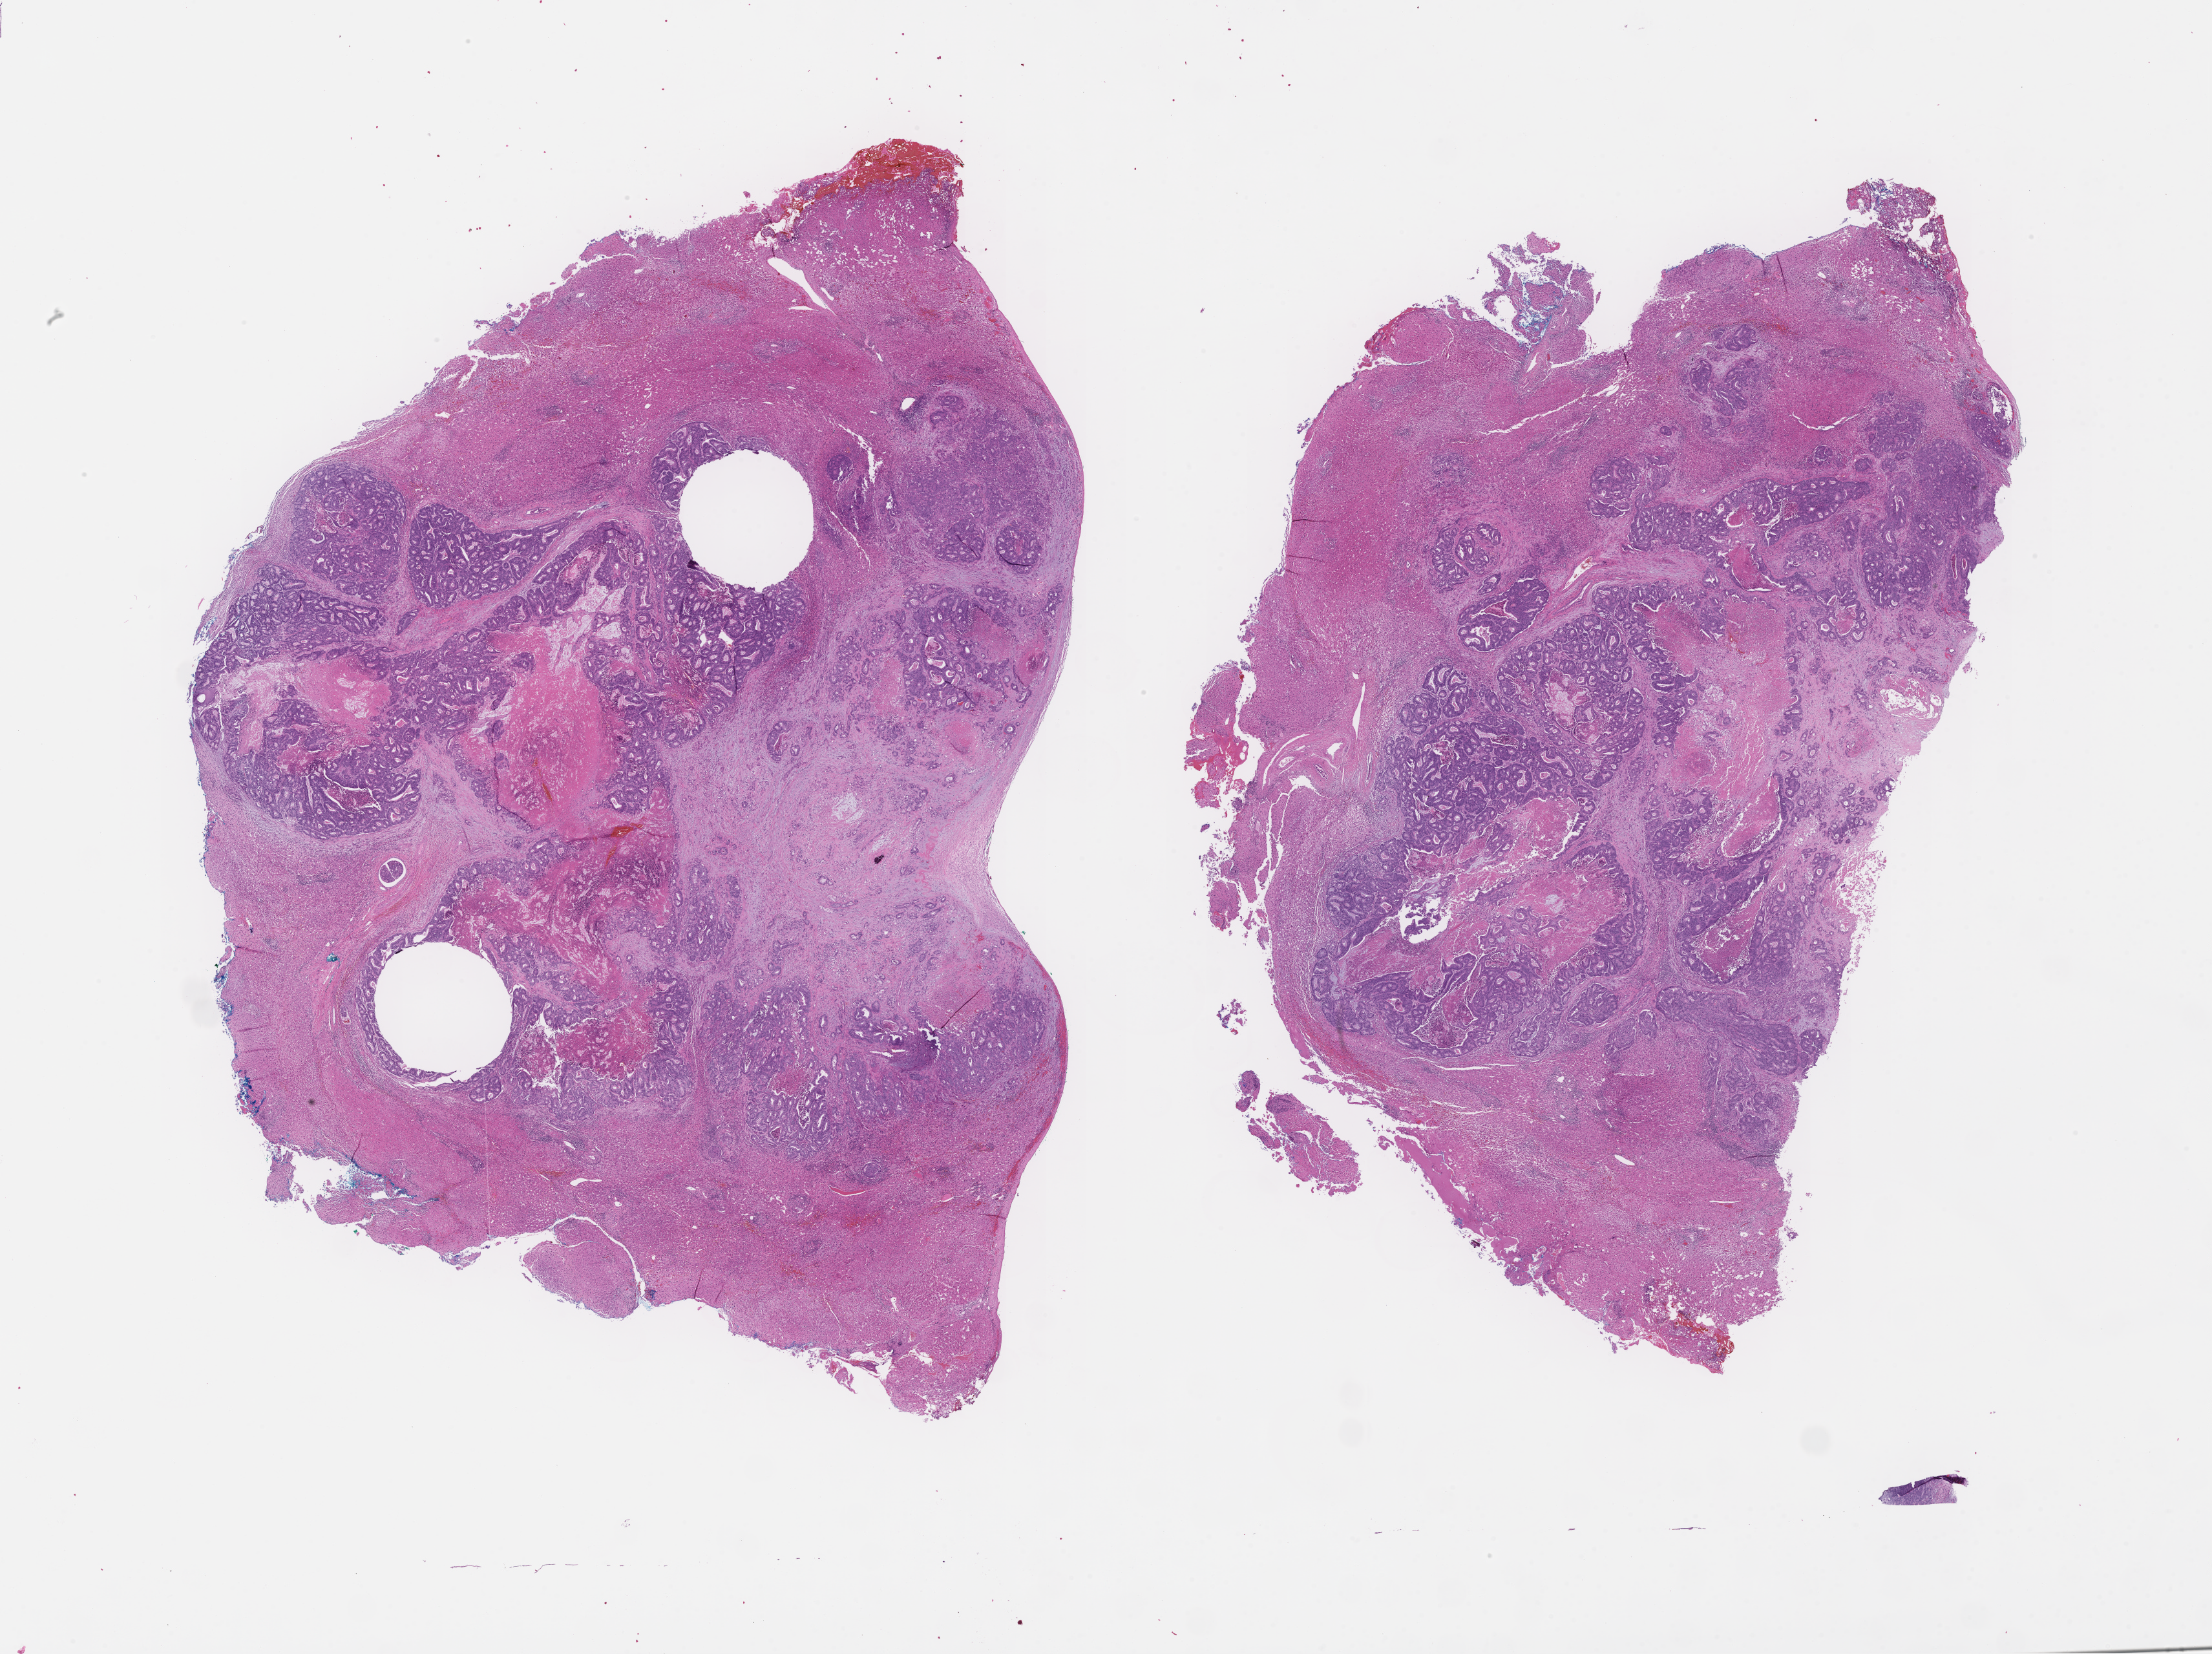
Haematoxylin and eosin whole-slide image — low-resolution overview of the scanned area, about 27.6 x 20.7 mm. Formalin-fixed paraffin-embedded section. Specimen time point: archival tissue. Patient: male.
* this section: metastasis (sampled organ not recorded)
* primary diagnosis of the patient: Colorectal Carcinoma